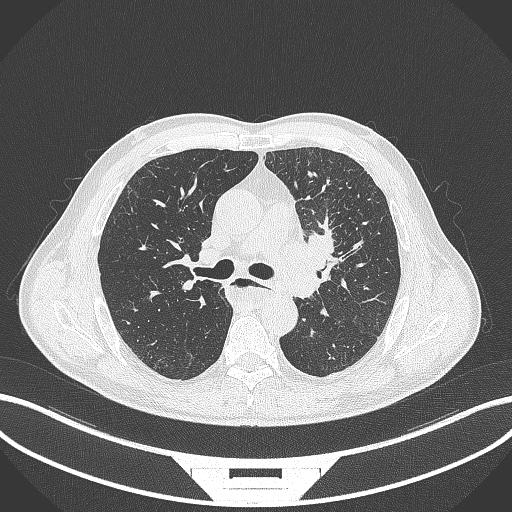
Chest CT, one axial slice. Position 236 of 411 along the scan axis. Lung window (W 1500 / L -600 HU). 1 mm slice thickness. 512 × 512 image matrix. Patient: male, 57 years. From the clinical record (not read from this slice): clinical TNM (as recorded): T2a N1 M0.
Annotated regions visible in this slice (rectangle marked by the reading radiologist):
- lung tumour (recorded histology: squamous cell carcinoma): bounding box <277,220,345,303> (left, top, right, bottom; pixels)